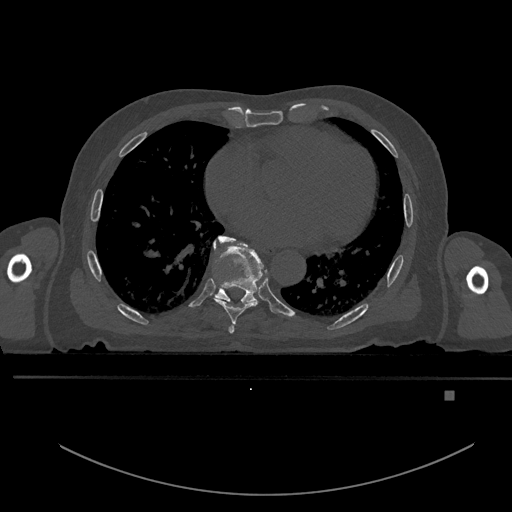
CT including the spine, one axial slice; slice 230 of 969 in the series (ordered by position); bone window (W 1800 / L 400 HU); 0.5 mm slice thickness; 512 × 512 image matrix, field of view 456 × 456 mm. Male patient, age 82 years. Case-level facts recorded for this patient, not image findings: primary cancer: prostate.
Annotated regions visible in this slice (semi-automatic segmentation, software-assisted and operator-edited):
- T6 vertebra: box from (x=228, y=325) to (x=234, y=333) px
- T7 vertebra: (x=215, y=235)–(x=268, y=324)
- T8 vertebra: (x=213, y=237)–(x=263, y=308)